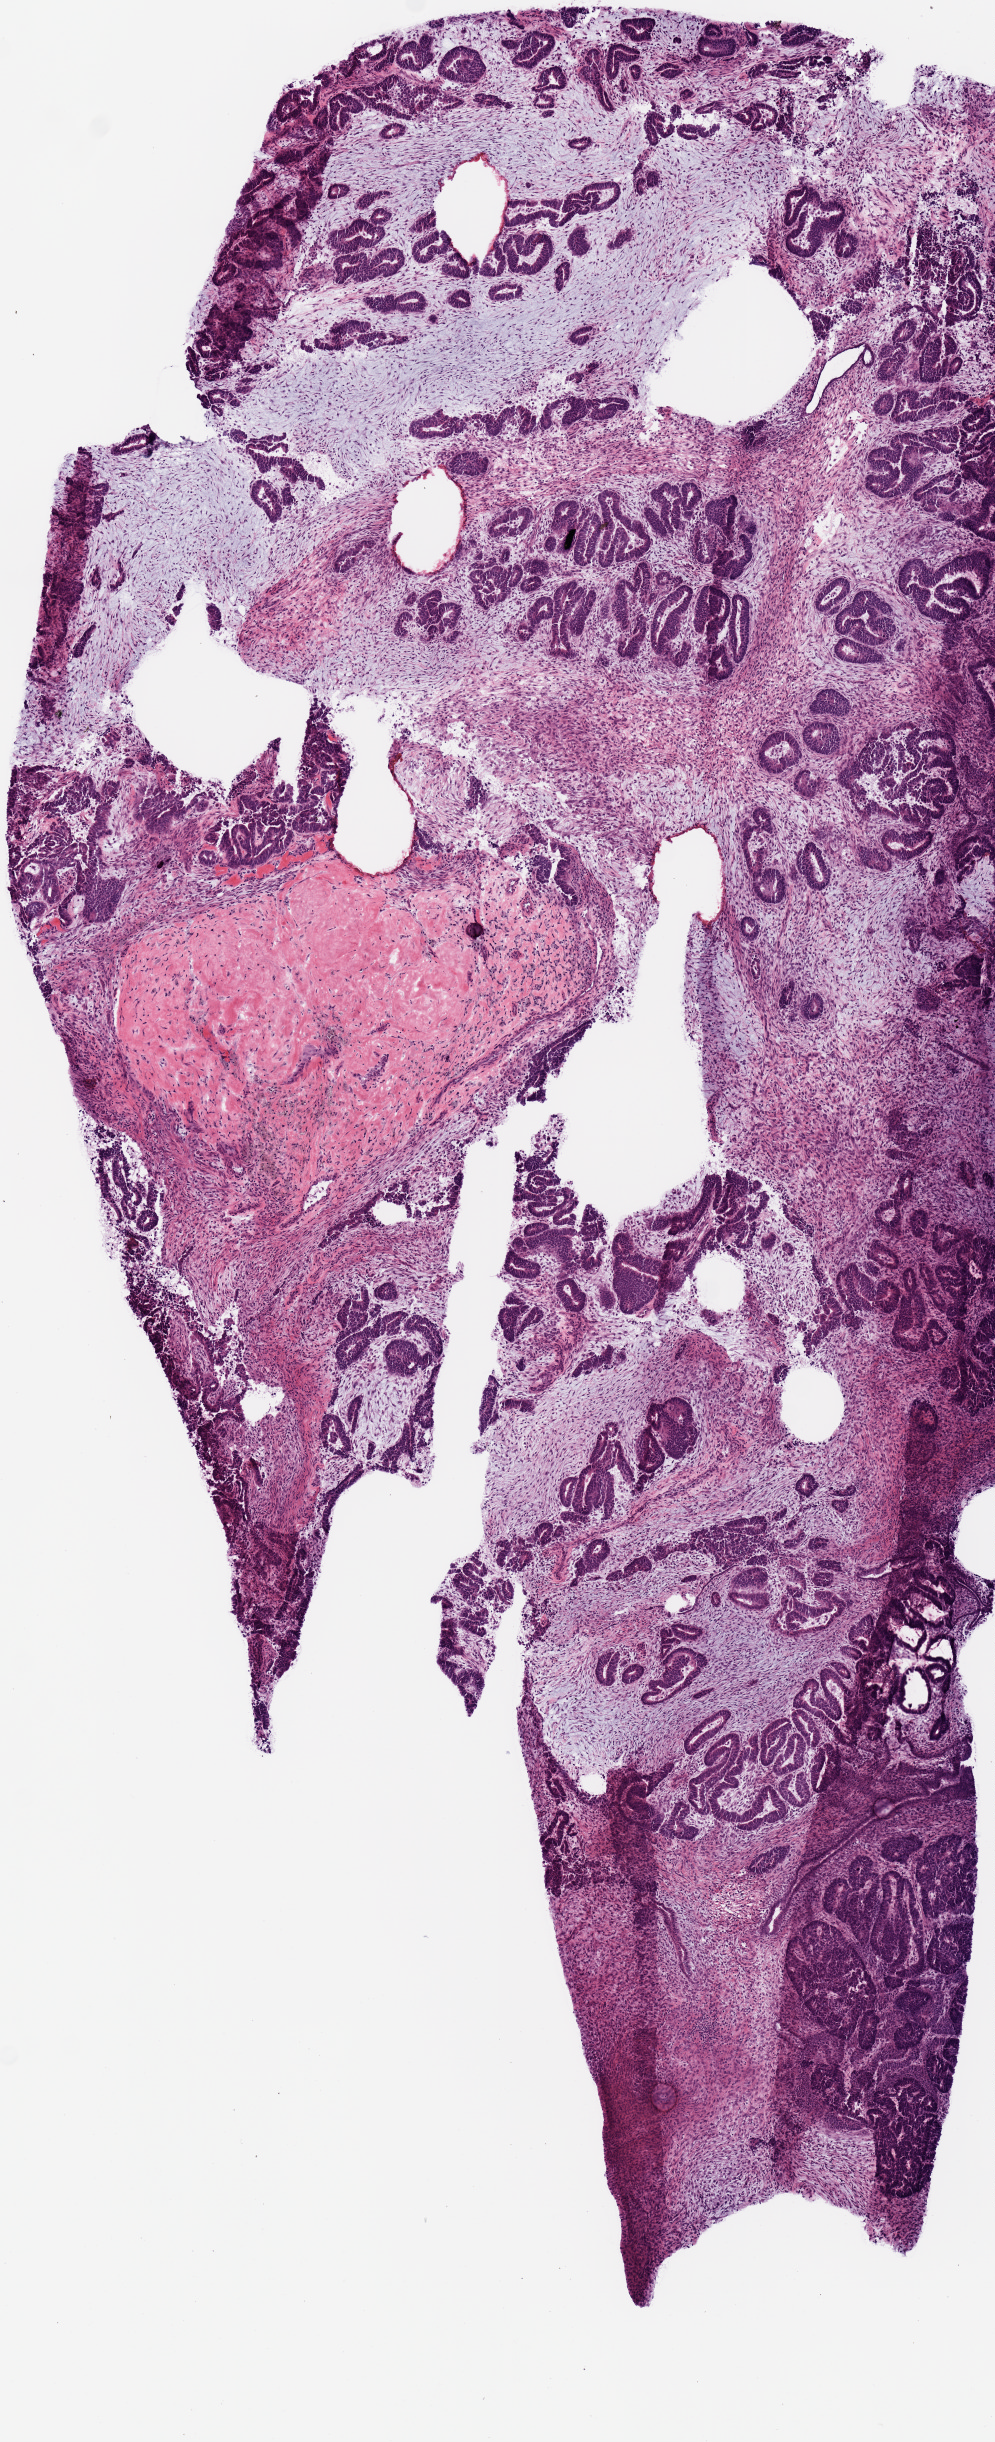
Digitized H&E tissue section (whole slide) — a low-resolution overview of the entire scanned area, about 3.9 x 9.7 mm. Frozen section from the top of the tissue portion. Primary tumour sample from the uterus. Female, age 61 years at initial diagnosis. Histologic grade: G3 (poorly differentiated). Composition of this section per pathologist review: tumour cells 90%, tumour nuclei 60%, normal cells 0%, stromal cells 10%, necrosis 0%. Infiltration values recorded for this section: lymphocyte infiltration 0%, monocyte infiltration 0%, neutrophil infiltration 0%.
* histologic diagnosis: Endometrioid adenocarcinoma, NOS (endometrium)
* FIGO stage: IA